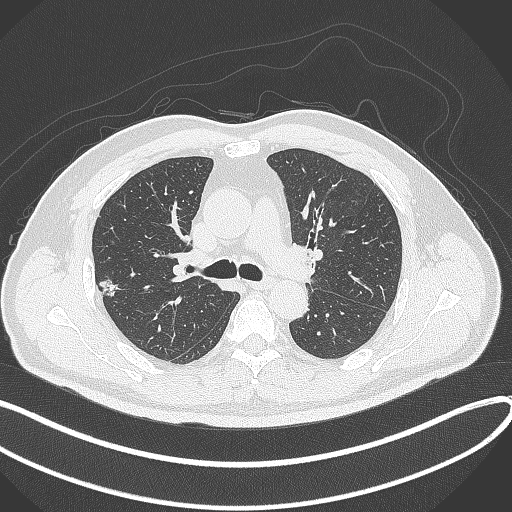
Chest CT, one axial slice. Slice 219 of 372 in the series (ordered by position). Reconstruction kernel B70f. 120 kVp. Lung window (W 1500 / L -600 HU). 1 mm slice thickness. 512 × 512 image matrix. Patient: male, 60 years. From the clinical record (not read from this slice): clinical TNM (as recorded): T1c N0 M0.
Annotated regions visible in this slice (bounding box drawn by a radiologist):
- lung tumour (recorded histology: adenocarcinoma): bounding box <96,273,126,299> (left, top, right, bottom; pixels)